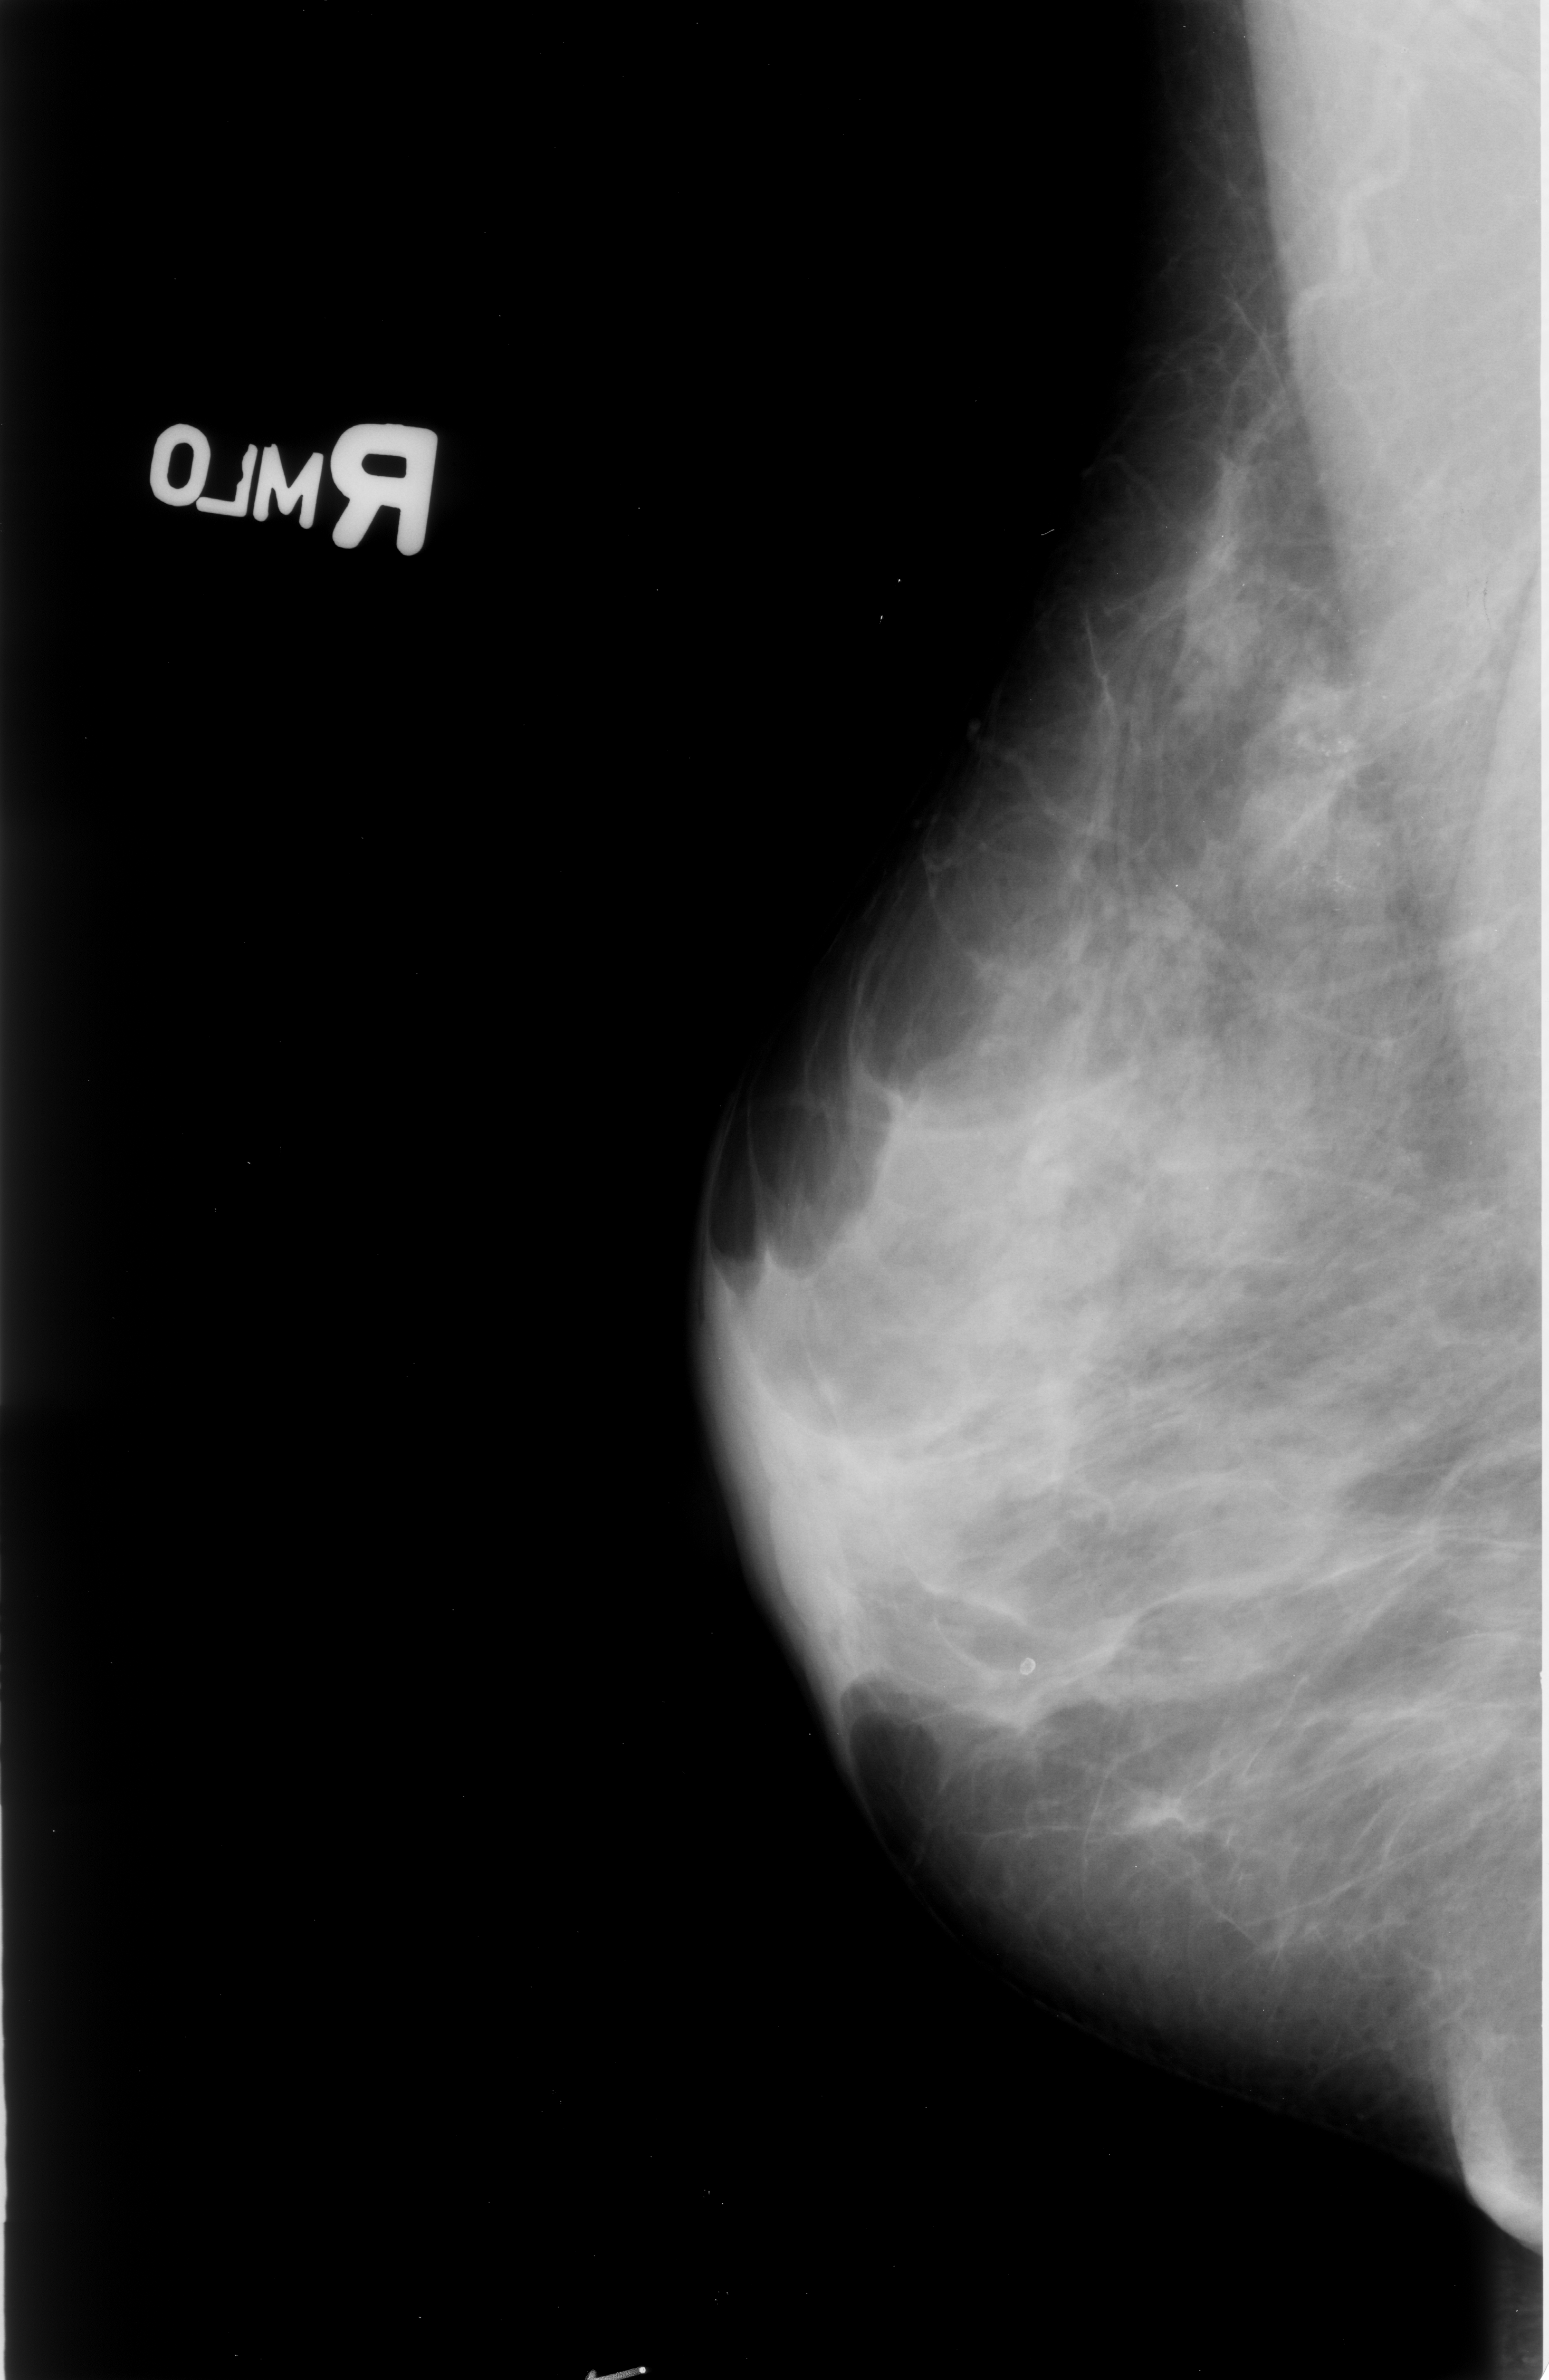
Mammogram (digitized film), right breast, MLO view, breast composition: heterogeneously dense (BI-RADS density category 3 of 4).
Finding: calcifications, morphology punctate / pleomorphic, distribution clustered; BI-RADS assessment category 4; subtlety rating 4 on a 1 (subtle) to 5 (obvious) scale; pathology (as recorded): malignant.